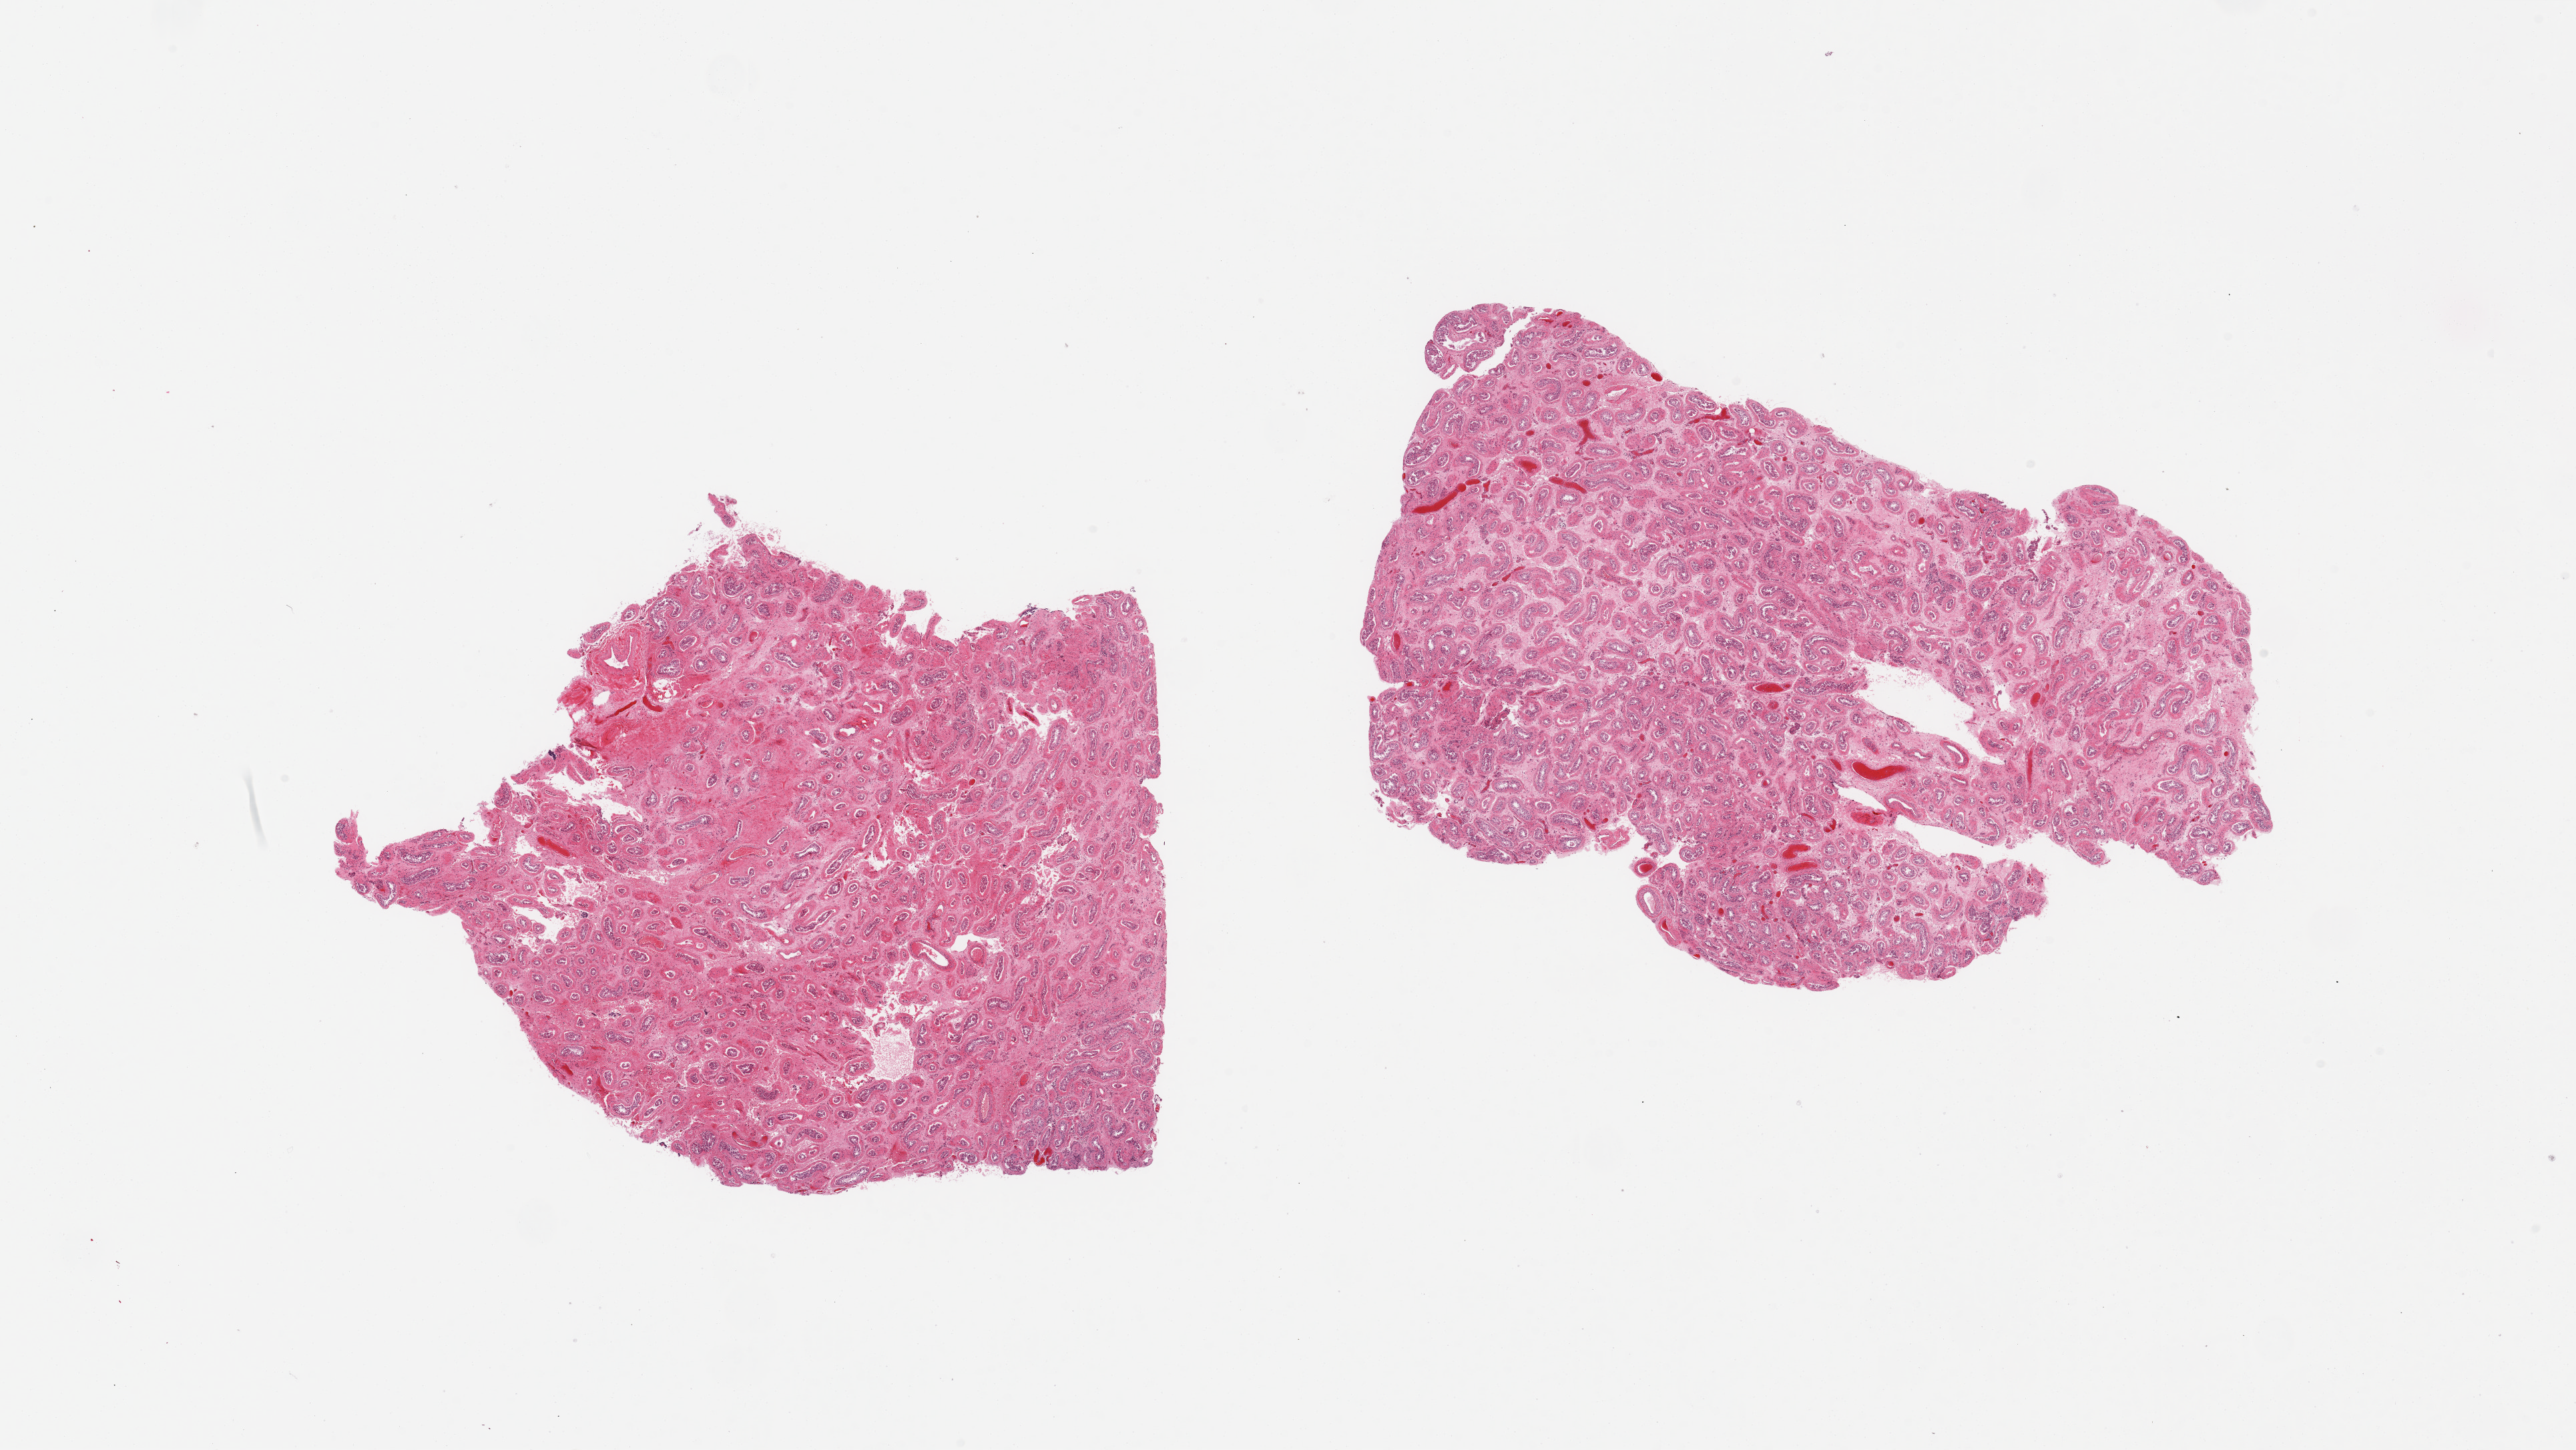
Digitized H&E-stained section — shown as a low-resolution overview of the whole scanned area (about 30.5 x 17.2 mm). PAXgene-fixed paraffin-embedded (PFPE) section. Section of testis (target tissue). Donor tissue sample. Donor sex: male.
• reviewer comment on this tissue sample: 2 pieces; atrophy with lack of spermatogenesis, thickening of tubular basement membrane, interstitial fibrosis; congestion